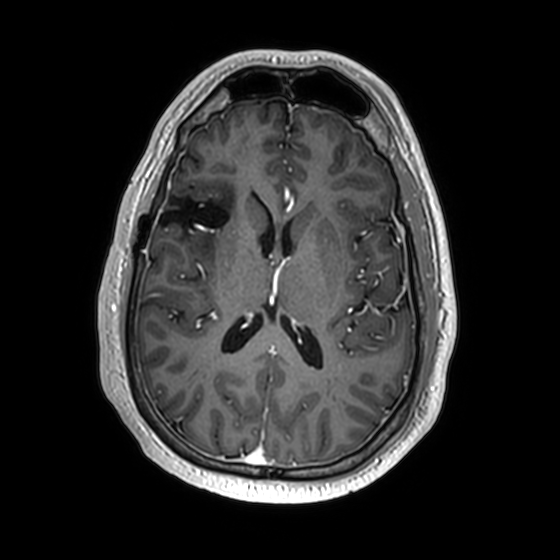
Brain MRI from a brain-tumour surgery series, one axial slice. Position 81 of 174 along the scan axis. T1-weighted post-contrast. 1 mm slice thickness. 560 × 560 image matrix, field of view 256 × 256 mm. From the clinical record (not read from this slice): histopathology: Astrocytoma; WHO grade: 2; IDH mutation: yes; tumour location: Right Insular.
Annotated regions visible in this slice (manually delineated by an expert):
- previous resection cavity: bounding box <159,196,229,228> (left, top, right, bottom; pixels)